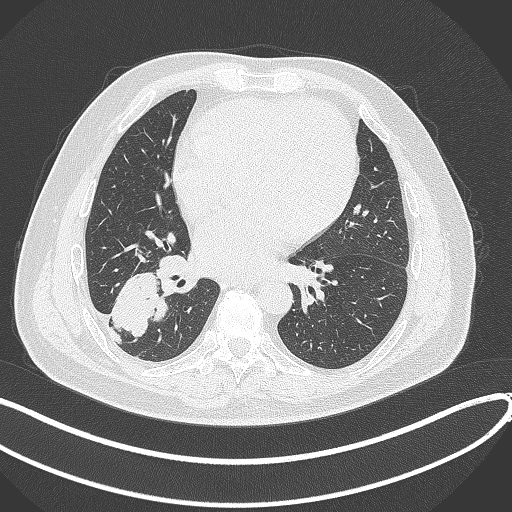
Chest CT, one axial slice. Position 156 of 360 along the scan axis. Reconstruction kernel B70f. 120 kVp. Lung window (W 1500 / L -600 HU). 1 mm slice thickness. 512 × 512 image matrix. Male patient, age 59 years.
Annotated regions visible in this slice (rectangle marked by the reading radiologist):
- lung tumour (recorded histology: adenocarcinoma): bounding box <109,266,170,340> (left, top, right, bottom; pixels)